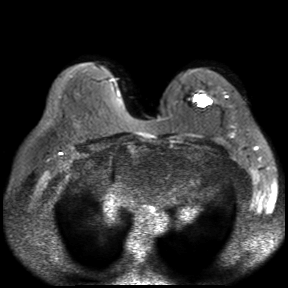
Breast MRI, one axial slice; position 17 of 30 along the scan axis; diffusion-weighted series; image 2 of 4 stored at this slice position (different b-values; order by instance number); 3 T; 288 × 288 image matrix, field of view 360 × 360 mm. Female patient.
Annotated regions visible in this slice (outlined manually by an expert reader):
- tumour on diffusion-weighted imaging: box from (x=199, y=98) to (x=211, y=107) px